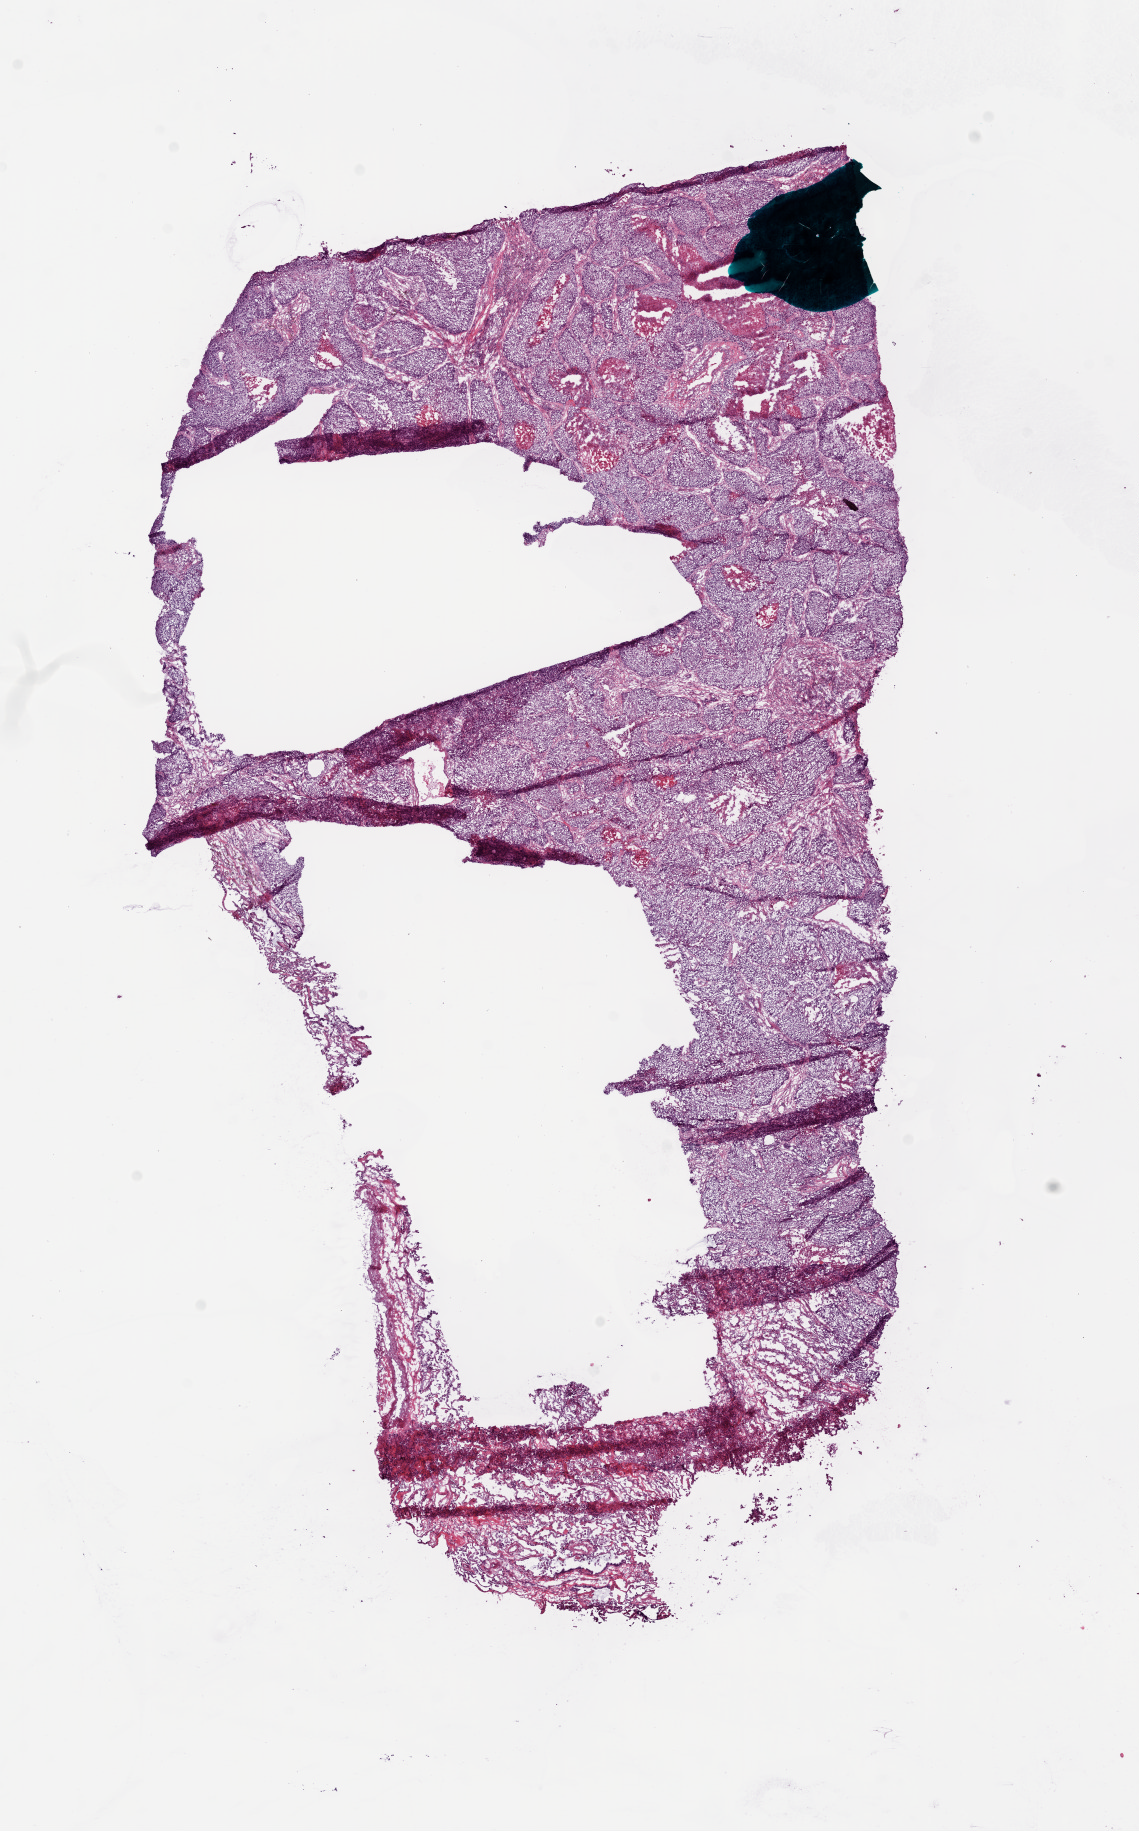
Hematoxylin and eosin (H&E) stained whole-slide image — whole scanned area (about 9.2 x 14.8 mm, from a 20x scan) shown as a low-resolution overview. Frozen section from the bottom of the tissue portion. Primary tumour sample from the lung. Patient: male, age at initial diagnosis 57 years.
Pathologic diagnosis: Squamous cell carcinoma, NOS (lower lobe, lung).